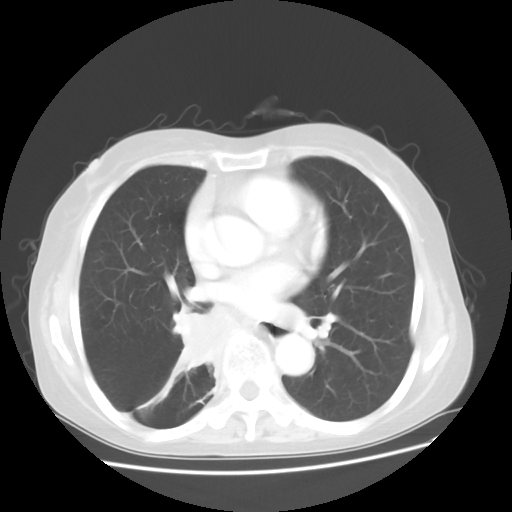
Chest CT, one axial slice. Slice 21 of 48 in the series (ordered by position). 120 kVp. Lung window (W 1500 / L -600 HU). 5 mm slice thickness. 512 × 512 image matrix, field of view 360 × 360 mm. Patient: female, 63 years. Case-level facts recorded for this patient, not image findings: clinical TNM (as recorded): T2 N3 M1b; histopathological grade: G3.
Outlined on this slice (bounding box drawn by a radiologist):
- lung tumour (recorded histology: small cell carcinoma): bounding box [x1, y1, x2, y2] px = [167, 300, 222, 377]